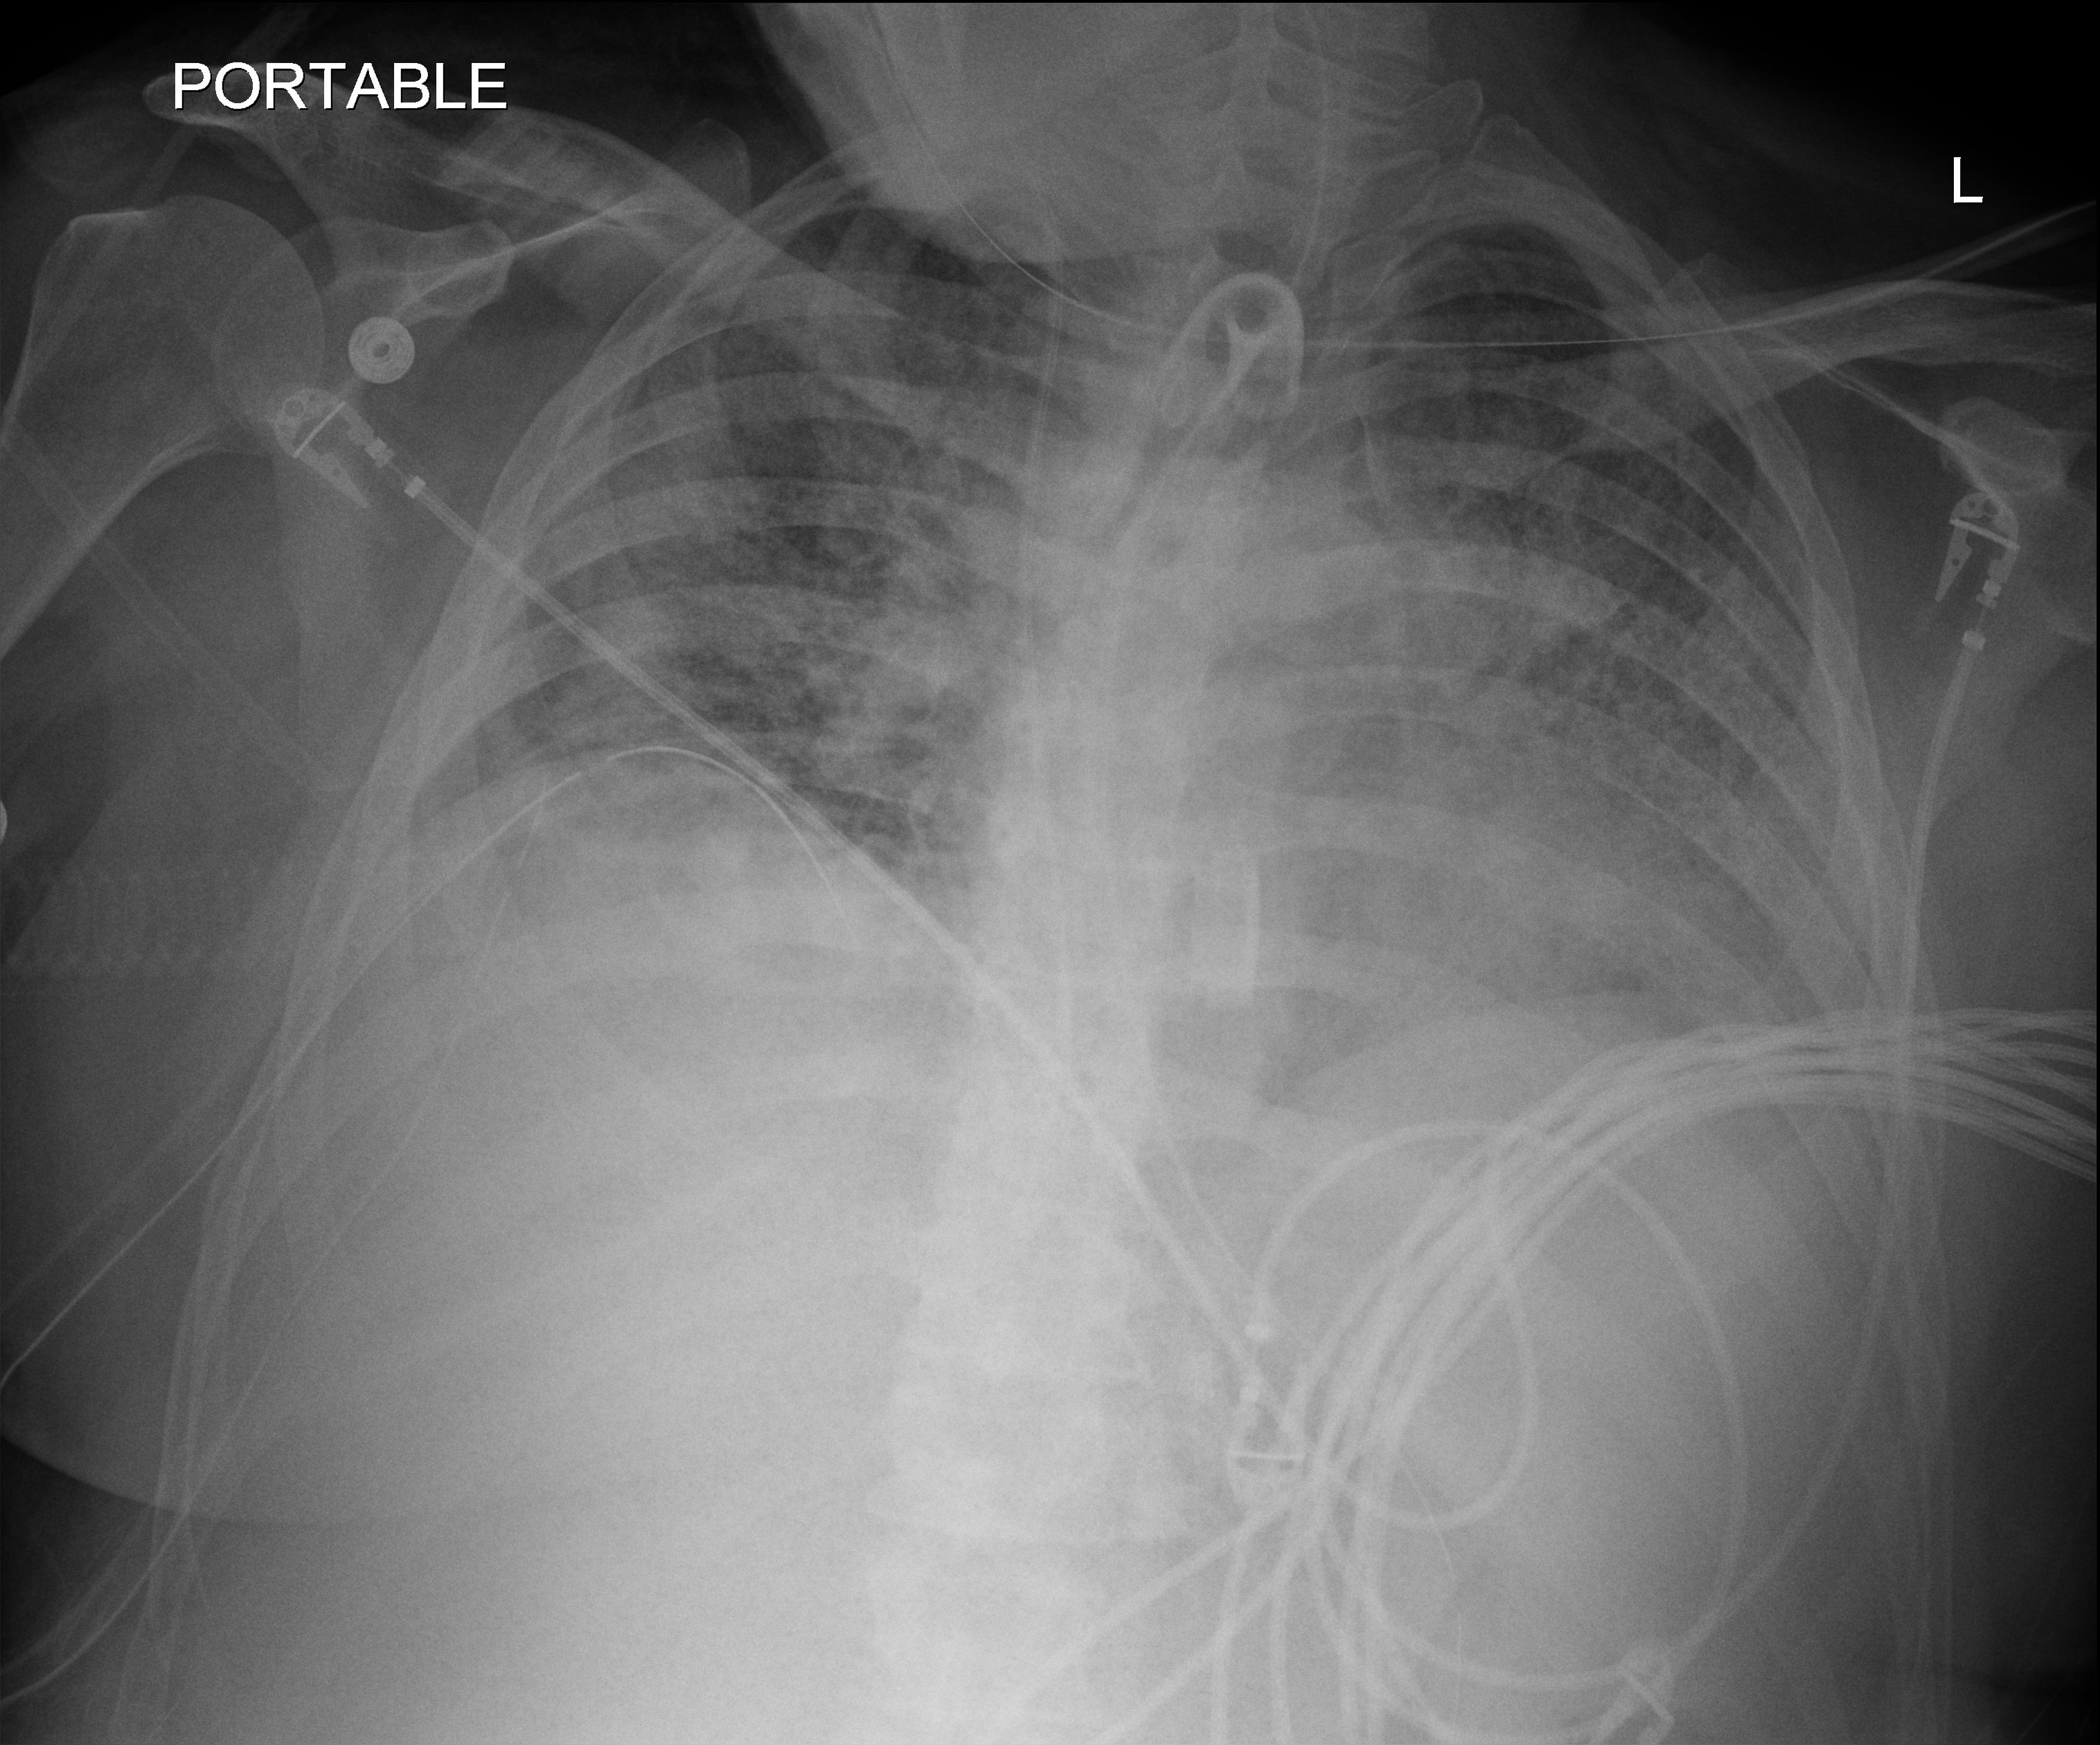
Bedside chest radiograph (digital radiography). Patient hospitalised with COVID-19; male, aged 18–59 years.
Admission-level facts for this patient (not findings on this image; timing relative to this image not recorded): mechanically ventilated during this hospital stay: yes.